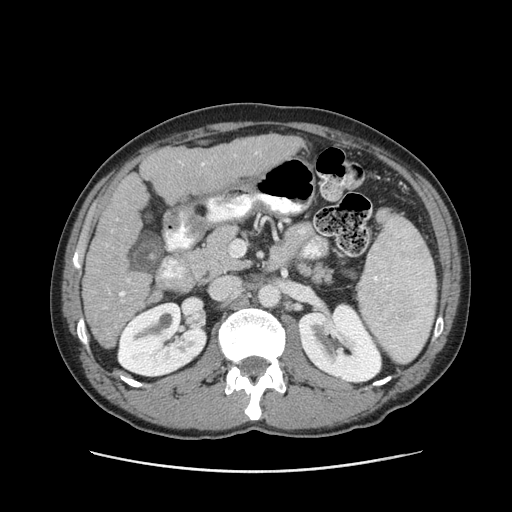
Contrast-enhanced abdominal CT (liver protocol), one axial slice; slice 41 of 93 in the series (ordered by position); reconstruction kernel STANDARD; soft-tissue window (W 400 / L 40 HU); 2.5 mm slice thickness; 512 × 512 image matrix. Case-level facts recorded for this patient, not image findings: diagnosis: hepatocellular carcinoma (patient treated with transarterial chemoembolisation; whether this scan precedes or follows treatment is not stated here); TNM stage (as recorded): Stage-II; Child-Pugh class: A; tumour differentiation: moderately differentiated; tumour size: 1 cm.
Annotated regions visible in this slice (semi-automatically segmented with operator editing):
- liver parenchyma outside the tumour (the mass and vessels are separate outlines, so this box may not span the whole liver): bounding box <82,134,304,348> (left, top, right, bottom; pixels)
- liver vessels: <105,152,257,308>